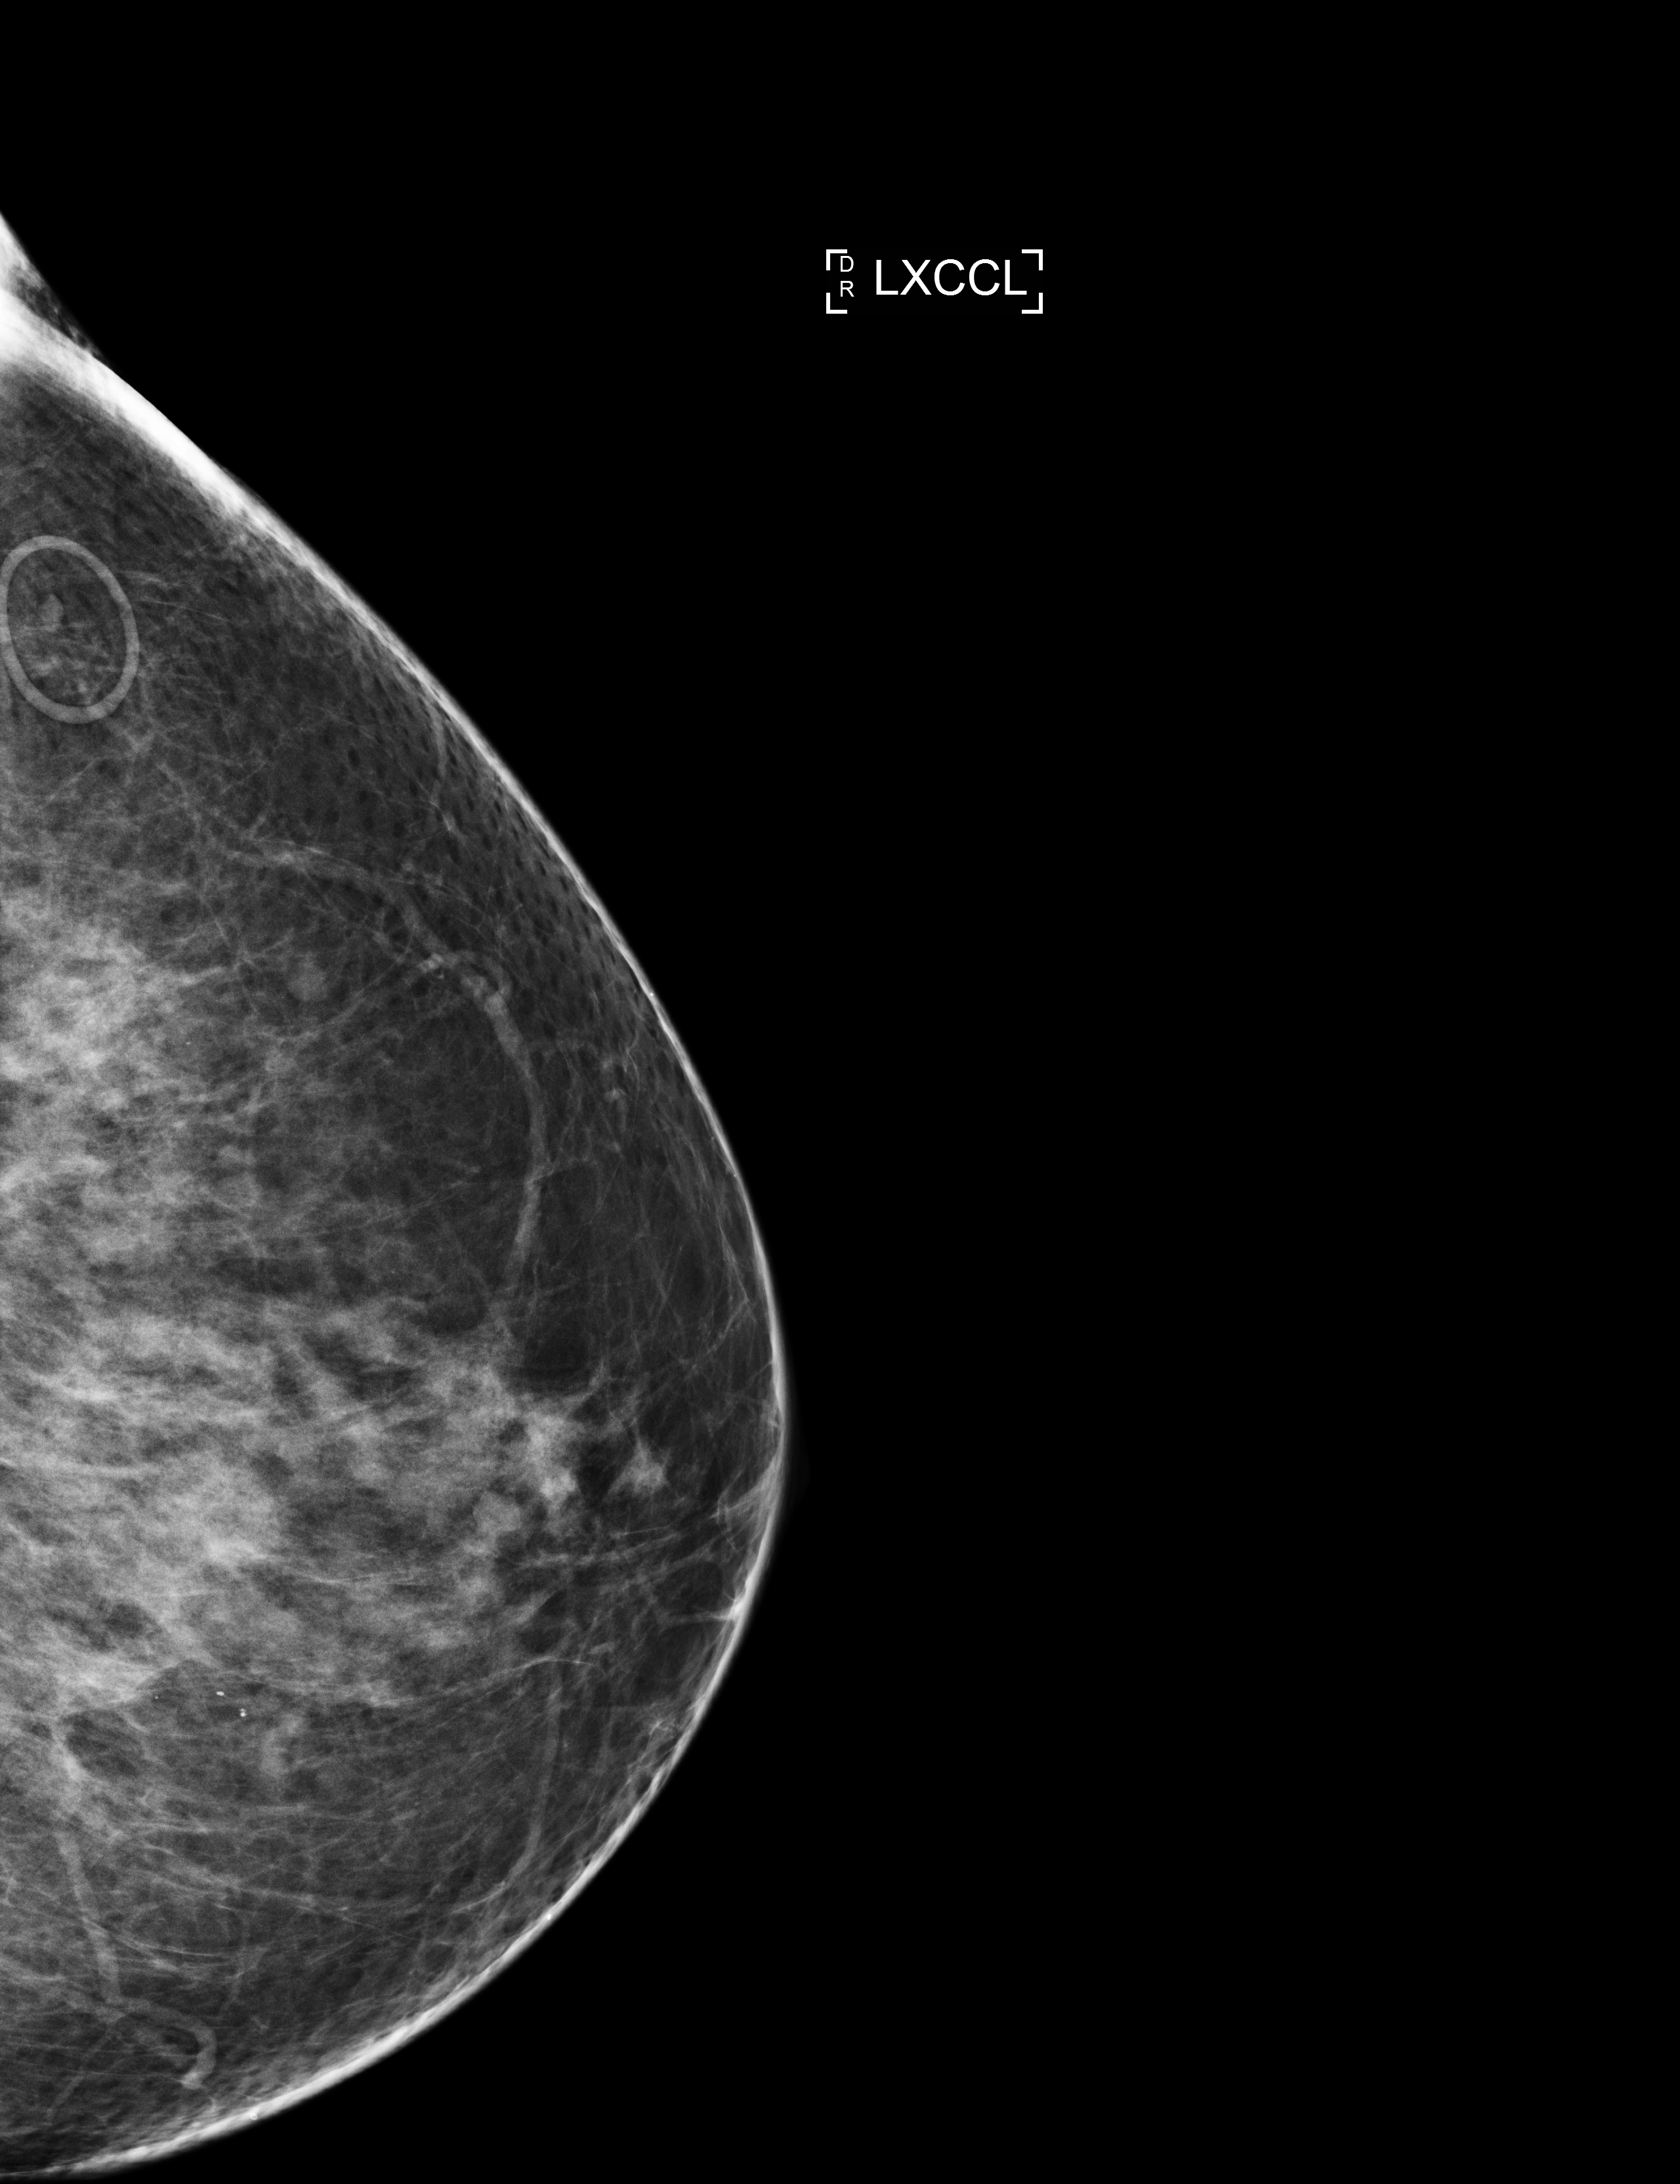
Full-field digital mammogram (FFDM), left breast, laterally exaggerated craniocaudal (XCCL) view, screening examination, compressed breast thickness 64 mm, system: Selenia Dimensions. Patient: female, 71 years.
- breast density at the screening exam (both breasts): heterogeneously dense (BI-RADS density category c)
- final BI-RADS category for the screening round (tomosynthesis exam, both breasts): category 2
- recall: recalled for additional imaging after this screen